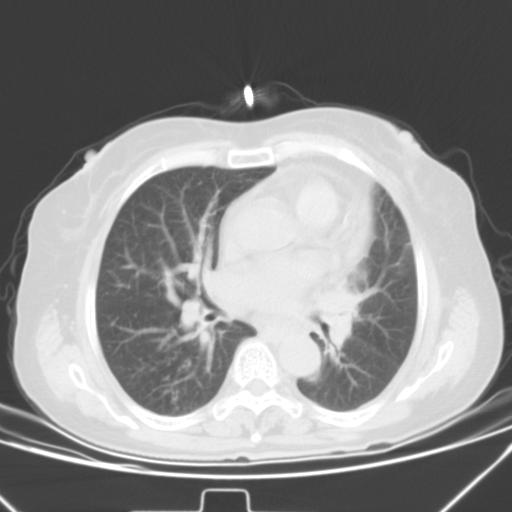
Chest CT, one axial slice; slice 23 of 42 in the series (ordered by position); 120 kVp; lung window (W 1500 / L -600 HU); 5 mm slice thickness; 512 × 512 image matrix, field of view 331 × 331 mm. Female patient, age 59 years. Case-level facts recorded for this patient, not image findings: clinical TNM (as recorded): T3 N1 M0.
Structures marked on this image (bounding box drawn by a radiologist):
- lung tumour (recorded histology: small cell carcinoma): bounding box <319,280,363,357> (left, top, right, bottom; pixels)